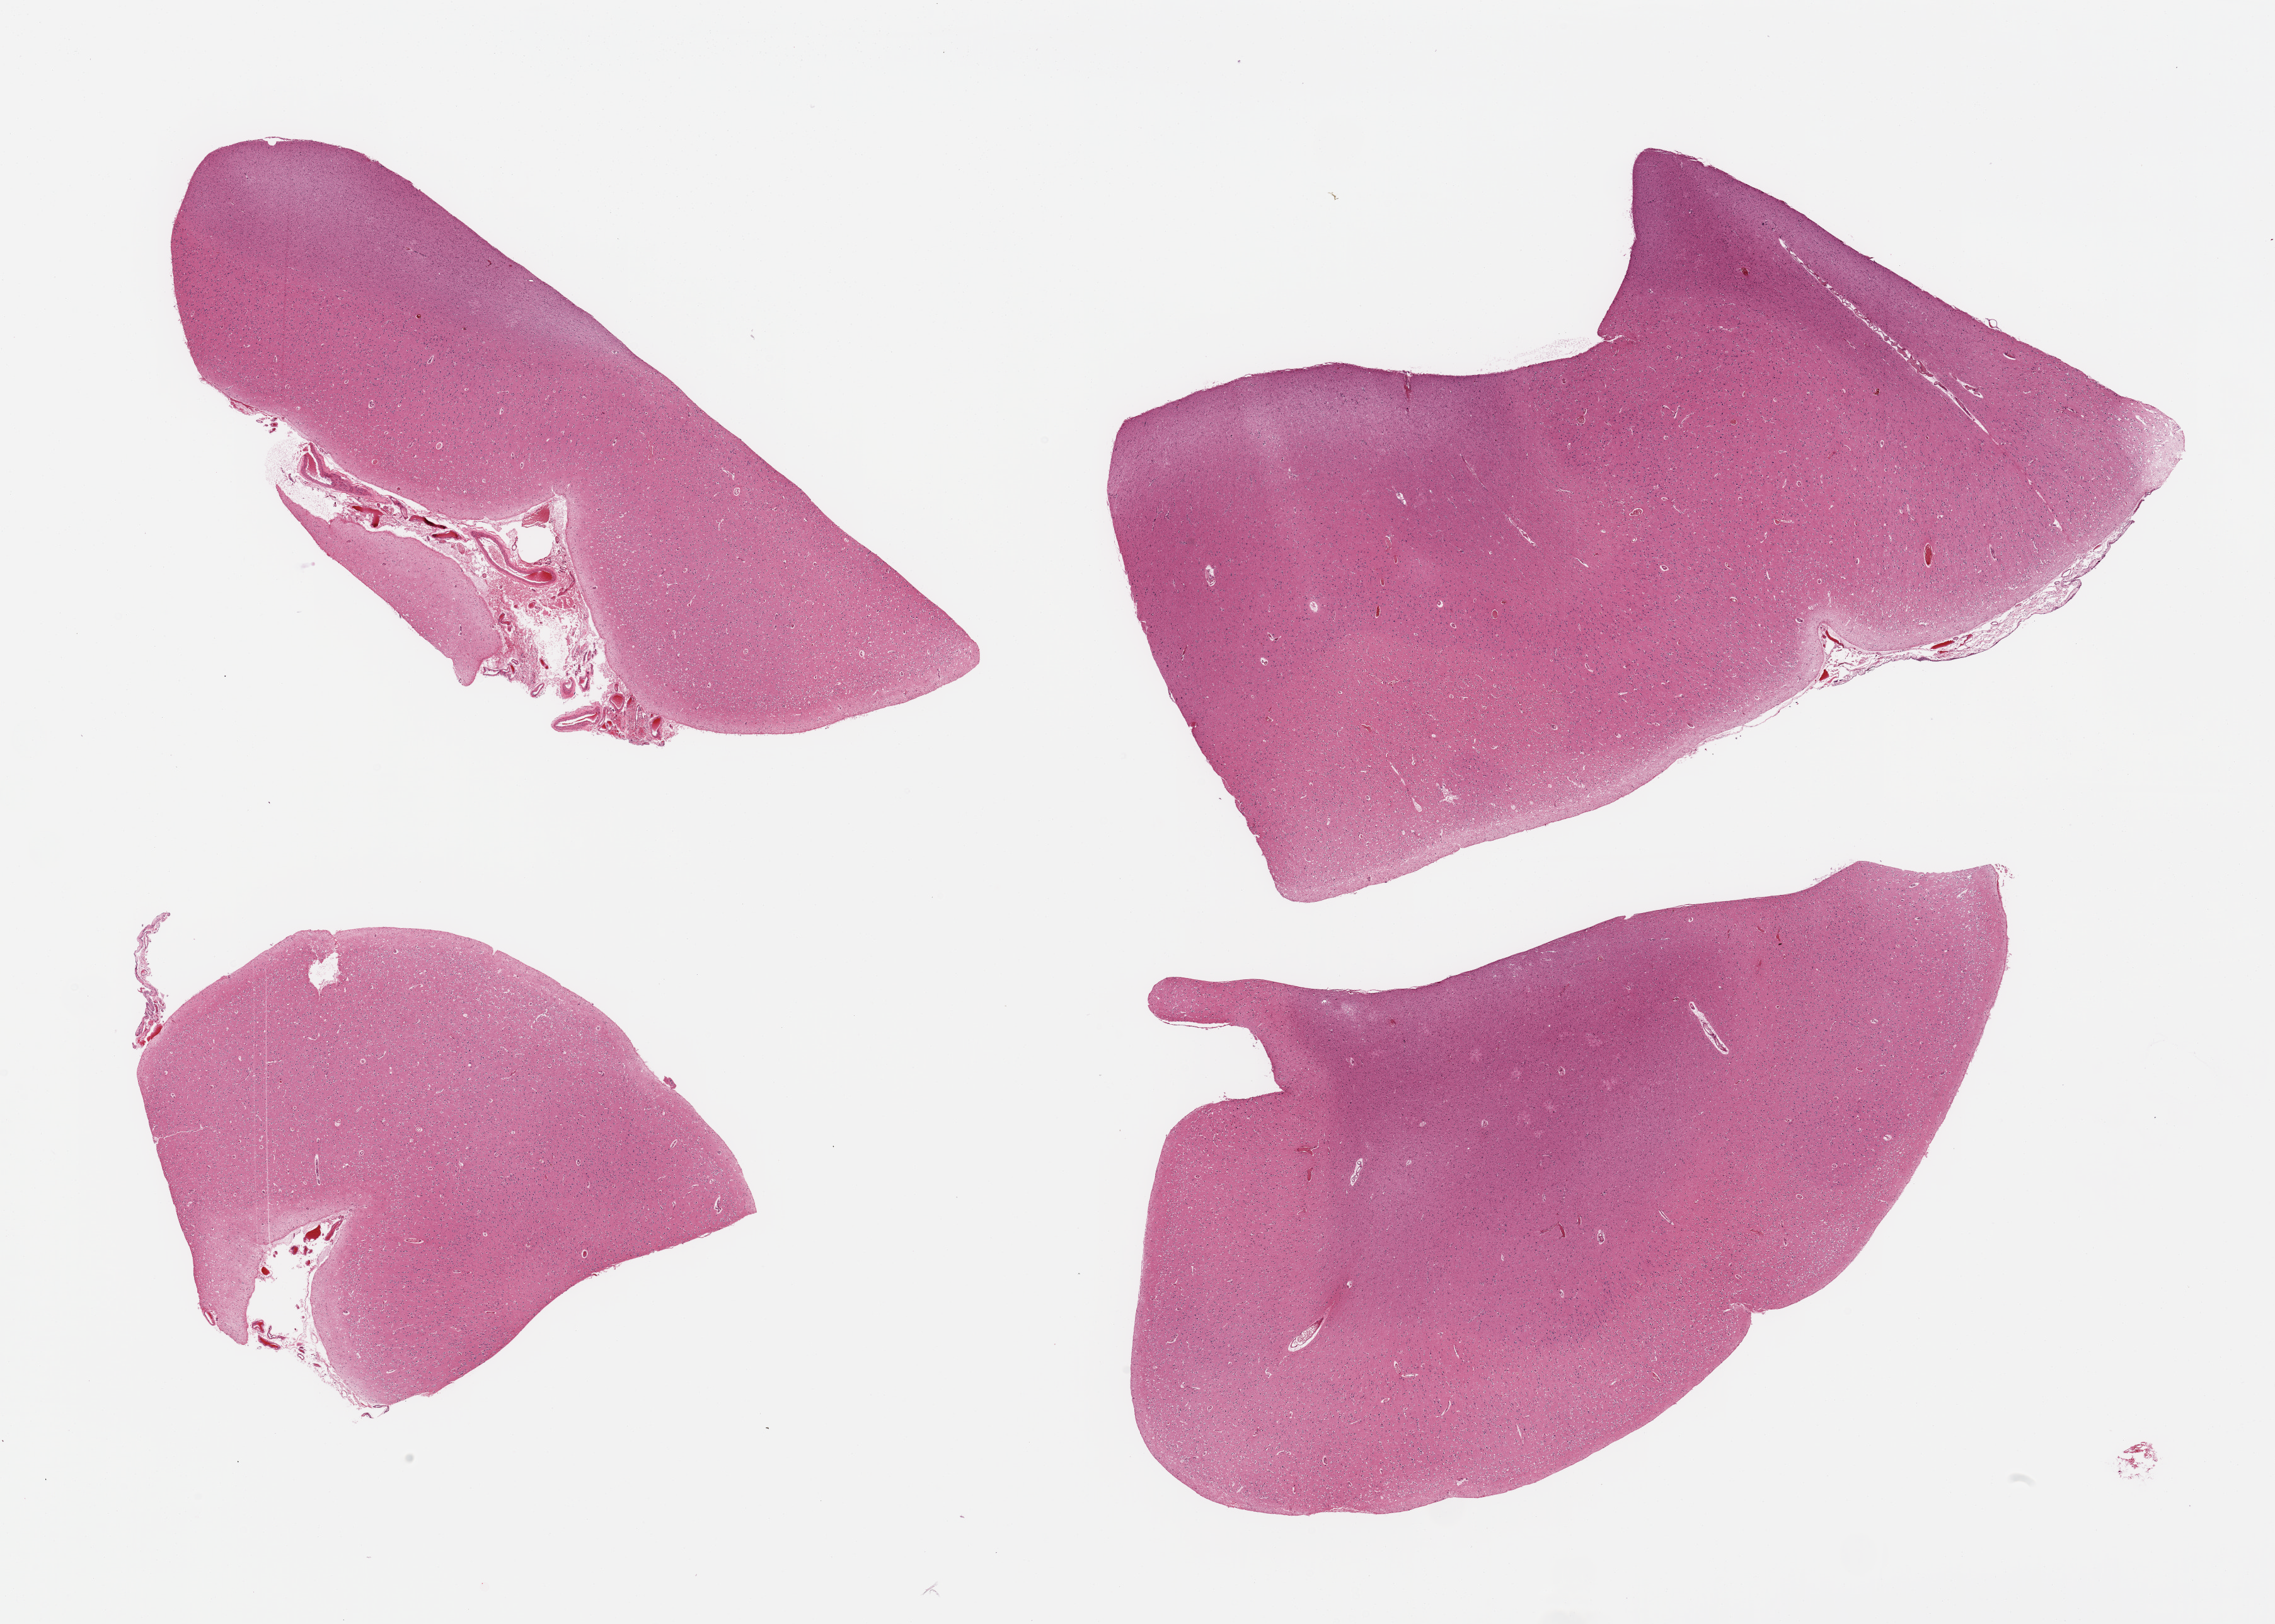
Whole-slide image, H&E stain — a low-resolution overview of the entire scanned area, about 28.5 x 20.4 mm (slide scanned at 20x), PAXgene-fixed, paraffin-embedded tissue, section of cerebral cortex (target tissue), donor tissue sample. Male donor.
* review note (as recorded): 4 pieces; 3 of 4 with congested meninges